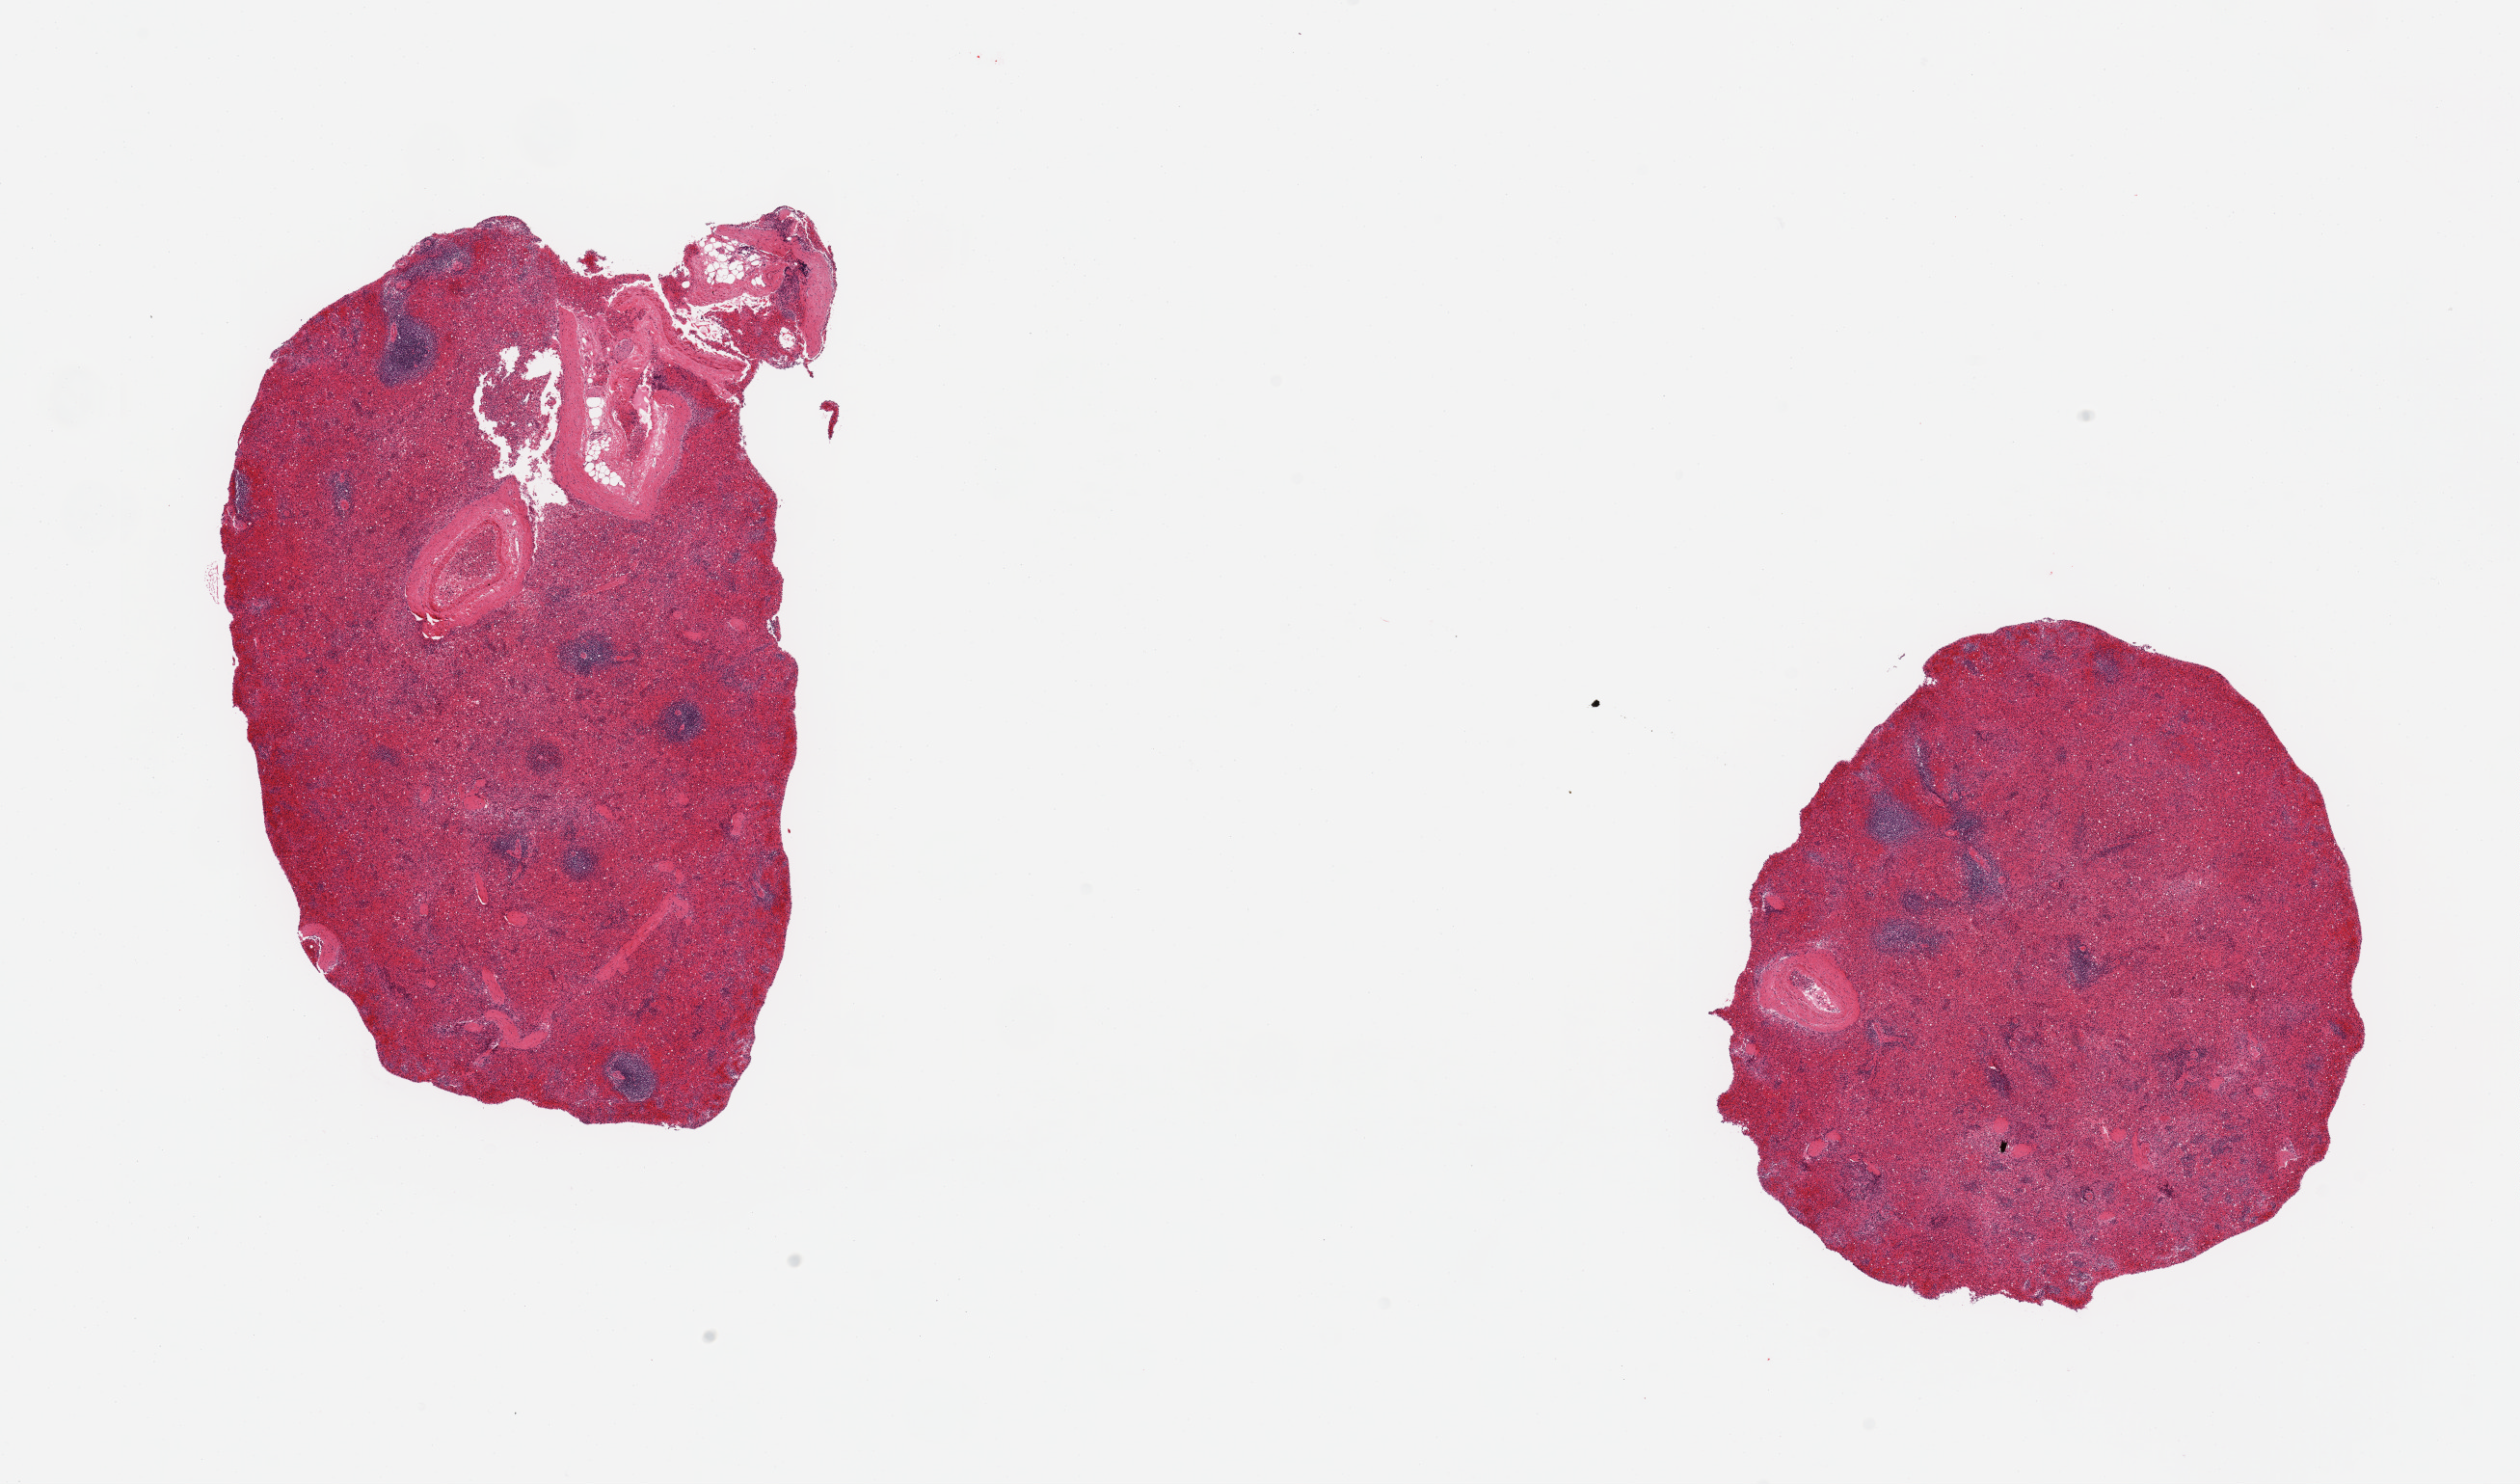
Haematoxylin and eosin whole-slide image, shown as a low-resolution overview of the whole scanned area (about 20.7 x 12.2 mm, acquisition: 20x scan); PAXgene-fixed paraffin-embedded (PFPE) section; sampled site (target tissue): spleen; tissue donor sample. Donor sex: male.
Pathologist's review note for this sample: 2 pieces; marked congestion; thick walled vessels 20% & 5% area.